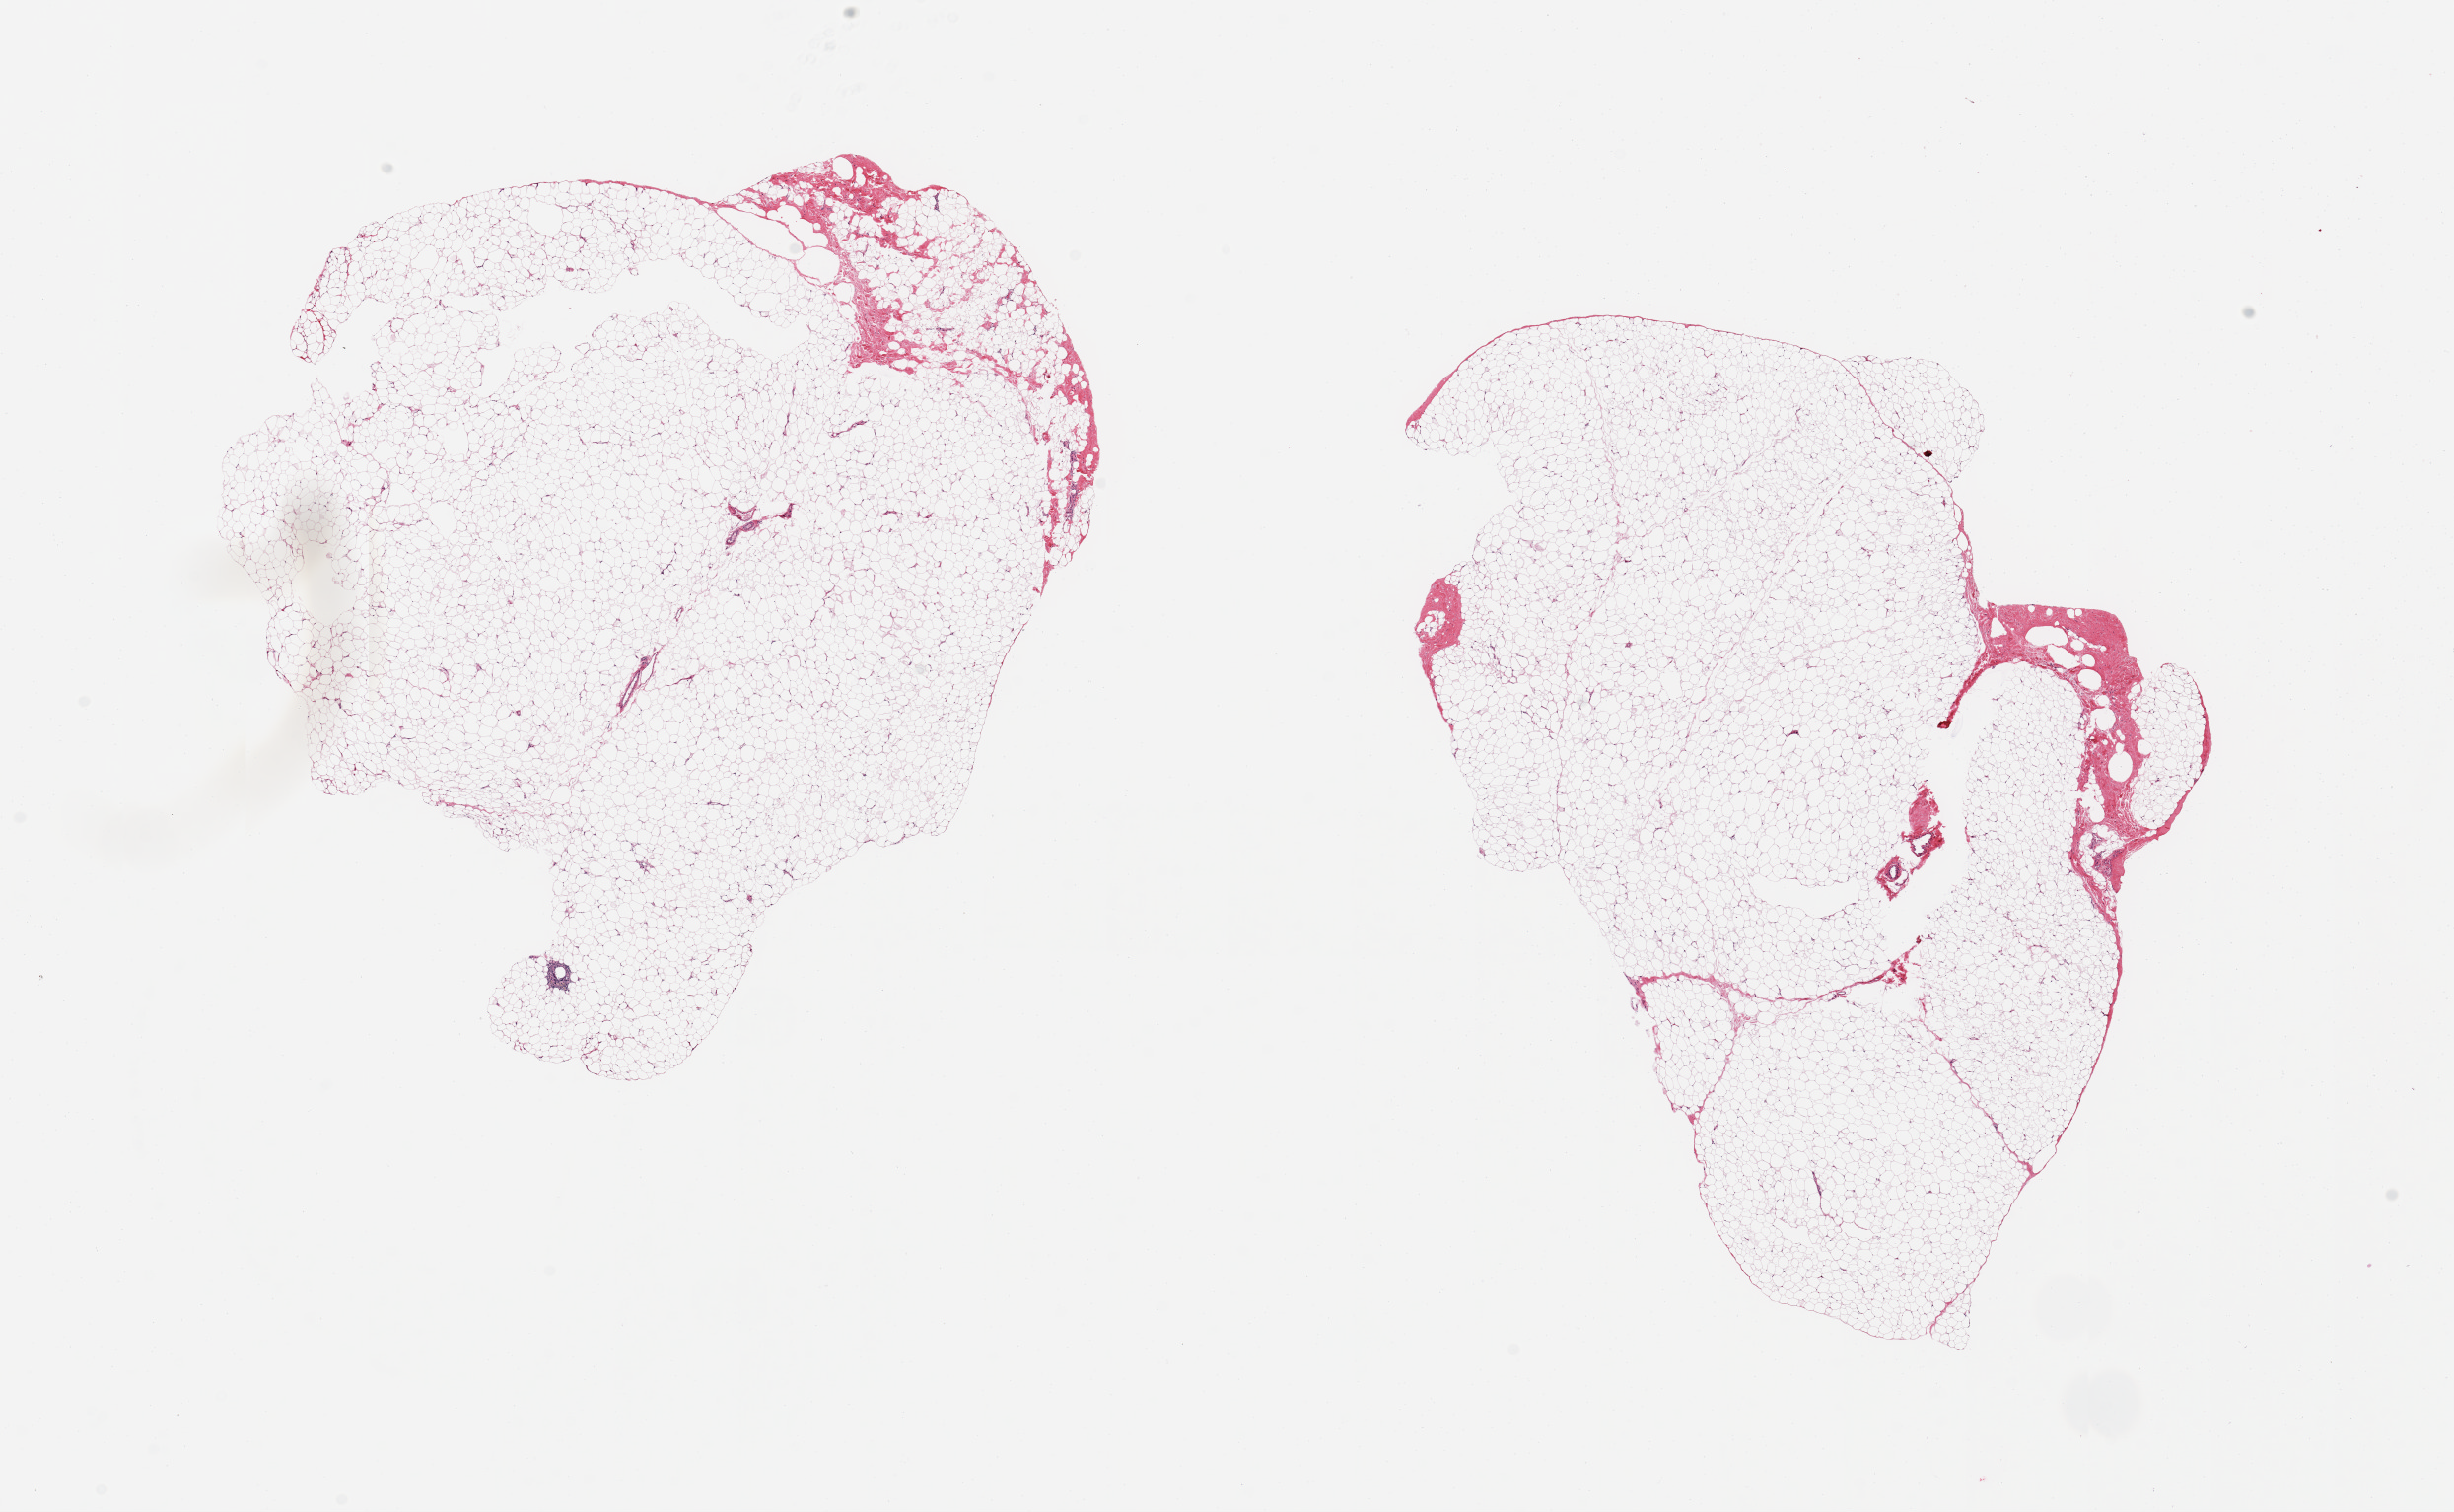
Haematoxylin and eosin whole-slide image, brightfield — low-resolution overview of the scanned area, about 19.7 x 12.1 mm (acquisition: 20x scan); PAXgene-fixed paraffin-embedded (PFPE) section; section of breast (target tissue); donor tissue sample. Male donor.
Reviewer comment on this tissue sample: 2 pieces, ~7x7mm;8x5mm; no mammary tissue, all fat and foci of fibrous stroma.